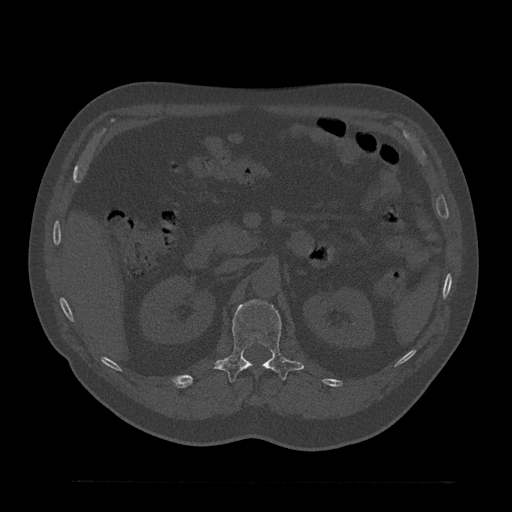
CT including the spine, one axial slice; slice 173 of 797 in the series (ordered by position); bone window (W 1800 / L 400 HU); 0.5 mm slice thickness; 512 × 512 image matrix, field of view 430 × 430 mm. Patient: male, 61 years. From the clinical record (not read from this slice): primary cancer: prostate.
Outlined on this slice (semi-automatically segmented with operator editing):
- L1 vertebra: bounding box <215,300,304,383> (left, top, right, bottom; pixels)